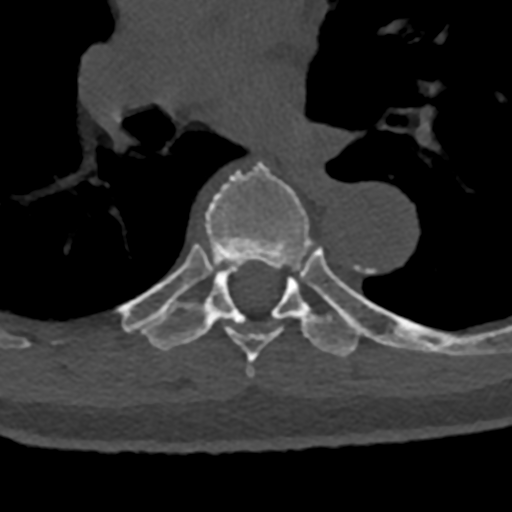
CT including the spine, one axial slice; slice 786 of 797 in the series (ordered by position); 120 kVp; bone window (W 1800 / L 400 HU); 0.5 mm slice thickness; 512 × 512 image matrix. Patient: male, 74 years. Case-level facts recorded for this patient, not image findings: primary cancer: renal; vertebrae with lytic lesions (as recorded): T10, L1, L2, L3, L4, L5.
Annotated regions visible in this slice (semi-automatic segmentation, software-assisted and operator-edited):
- T6 vertebra: bounding box [x1, y1, x2, y2] px = [165, 161, 311, 378]
- T7 vertebra: [122, 246, 430, 358]